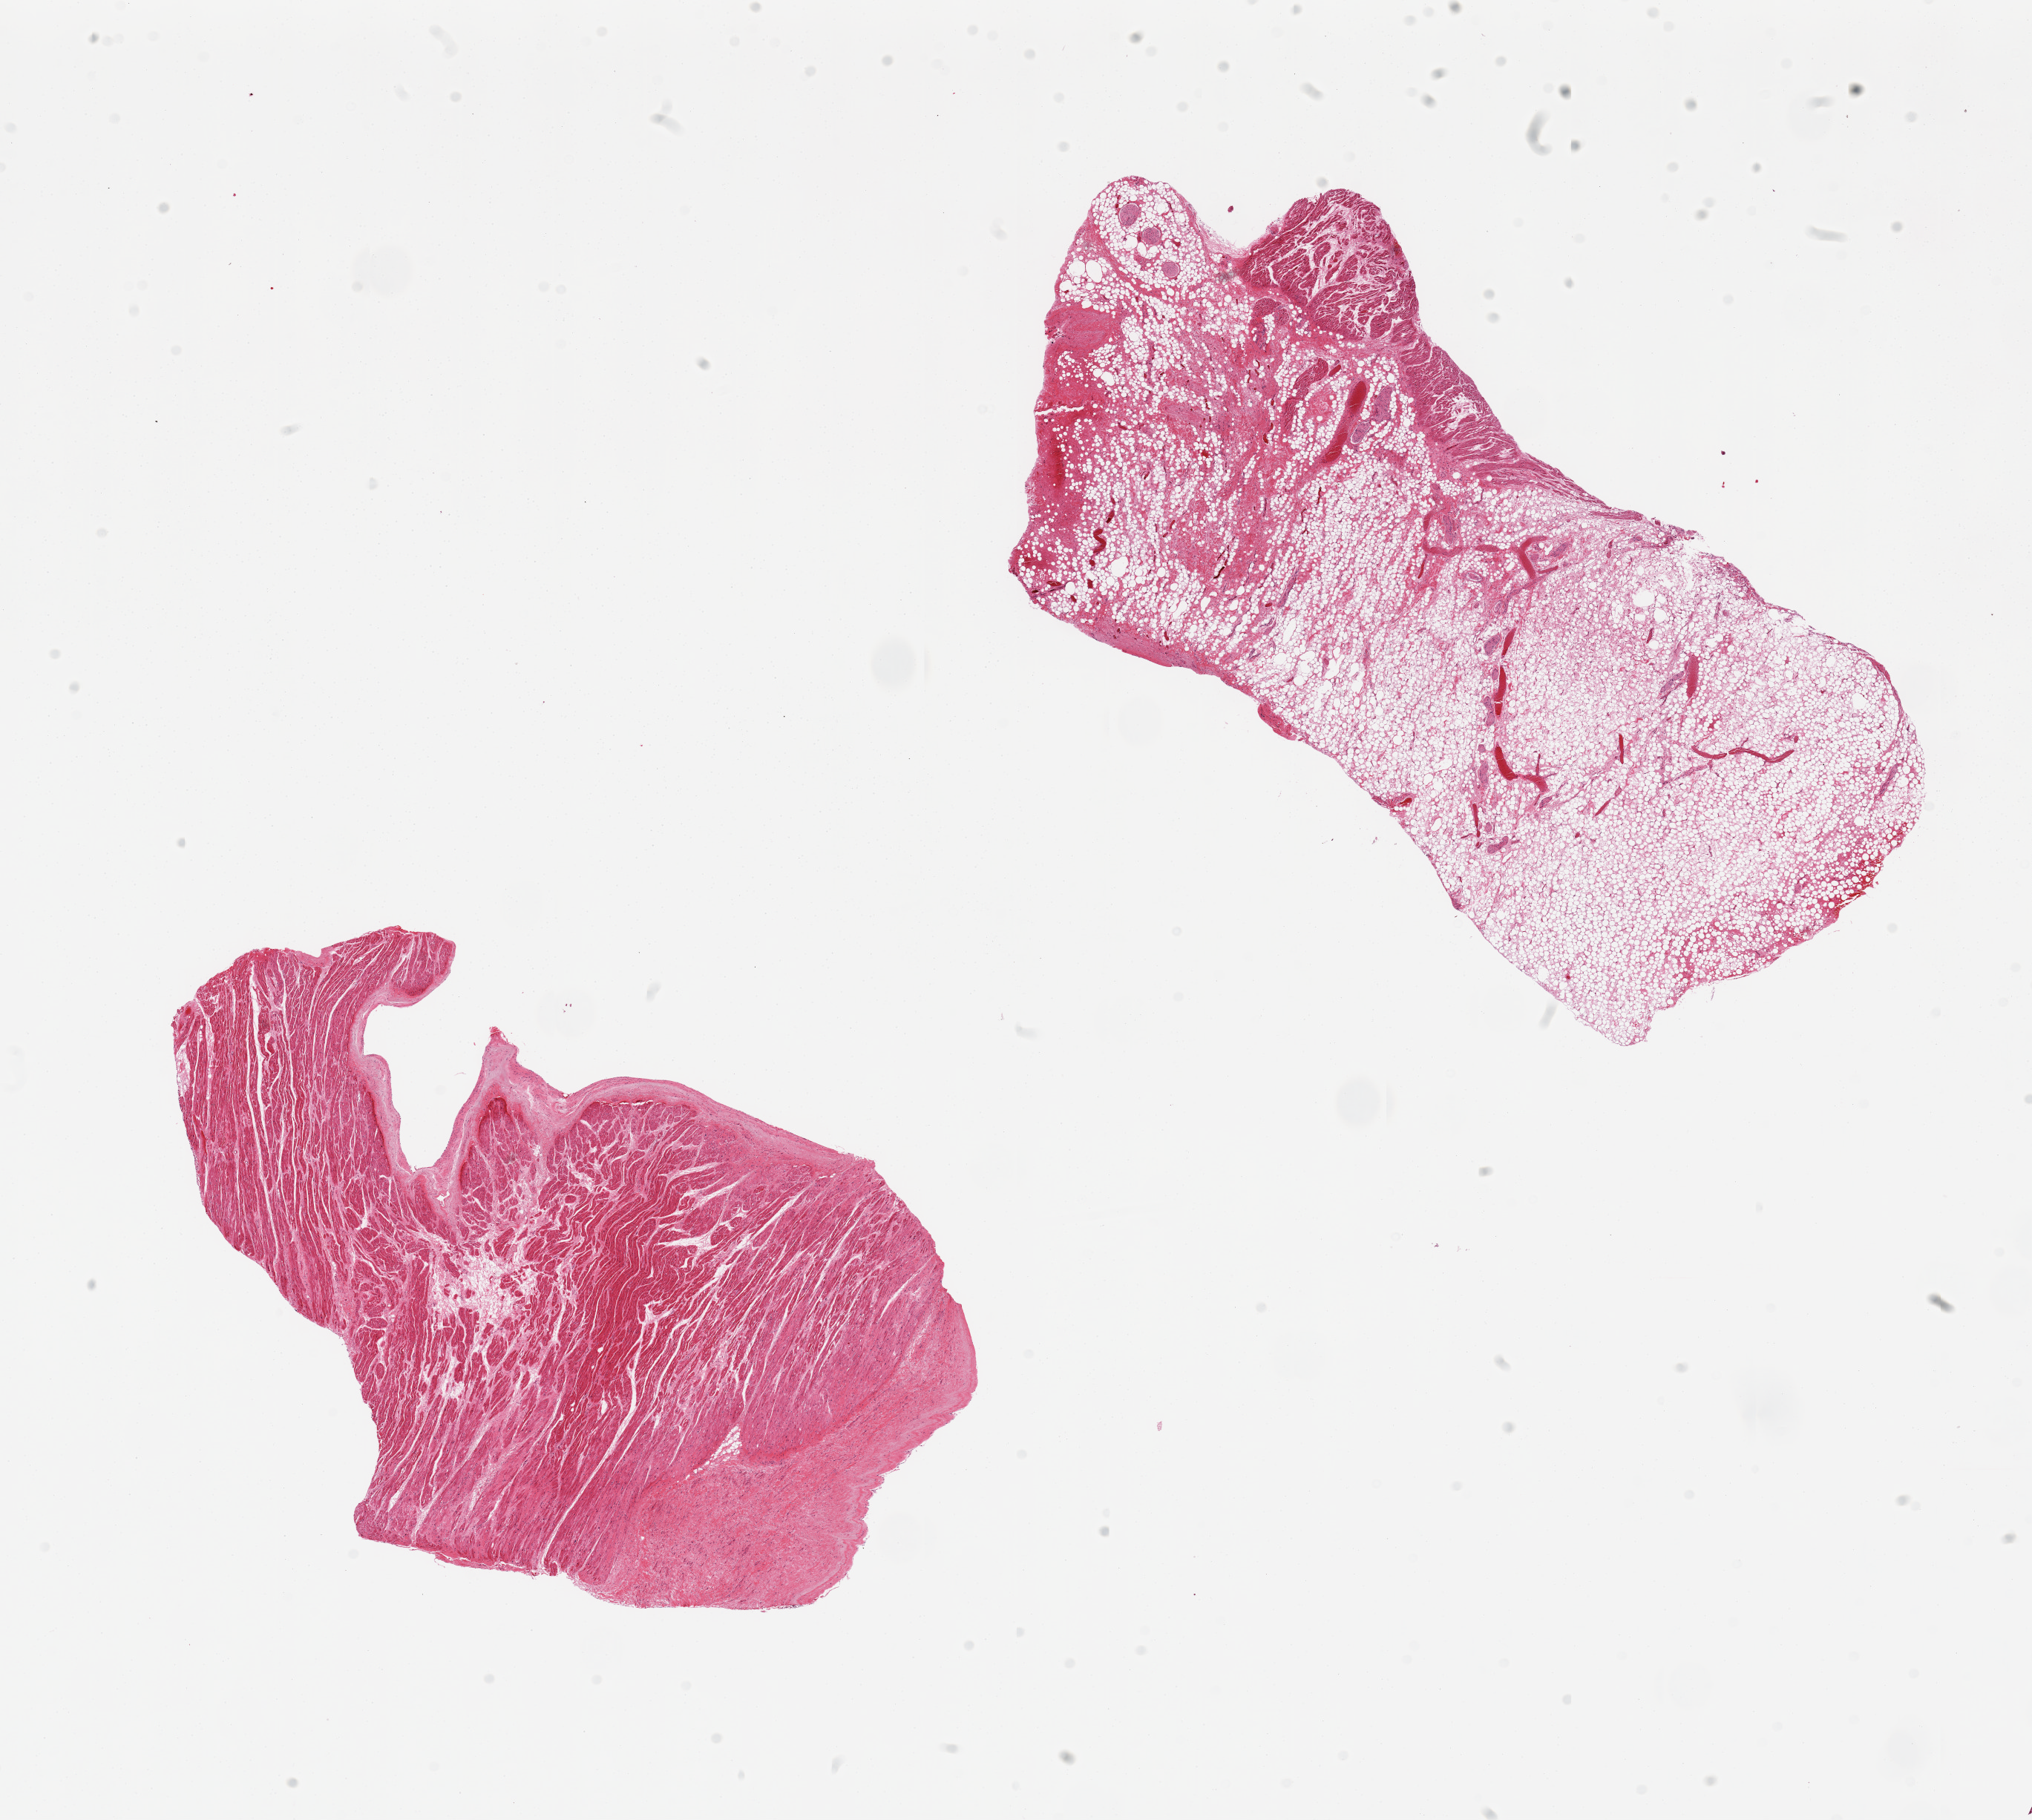
Haematoxylin and eosin whole-slide image, a low-resolution overview of the entire scanned area, about 21.7 x 19.4 mm; PAXgene-fixed paraffin-embedded (PFPE) section; sampled site (target tissue): auricular appendage; tissue donor sample. Donor: male.
Review note (as recorded): 2 pieces, one is predominantly fat and fibrous tissue with only ~10% cardiac muscle, second is ~30% fibrous.